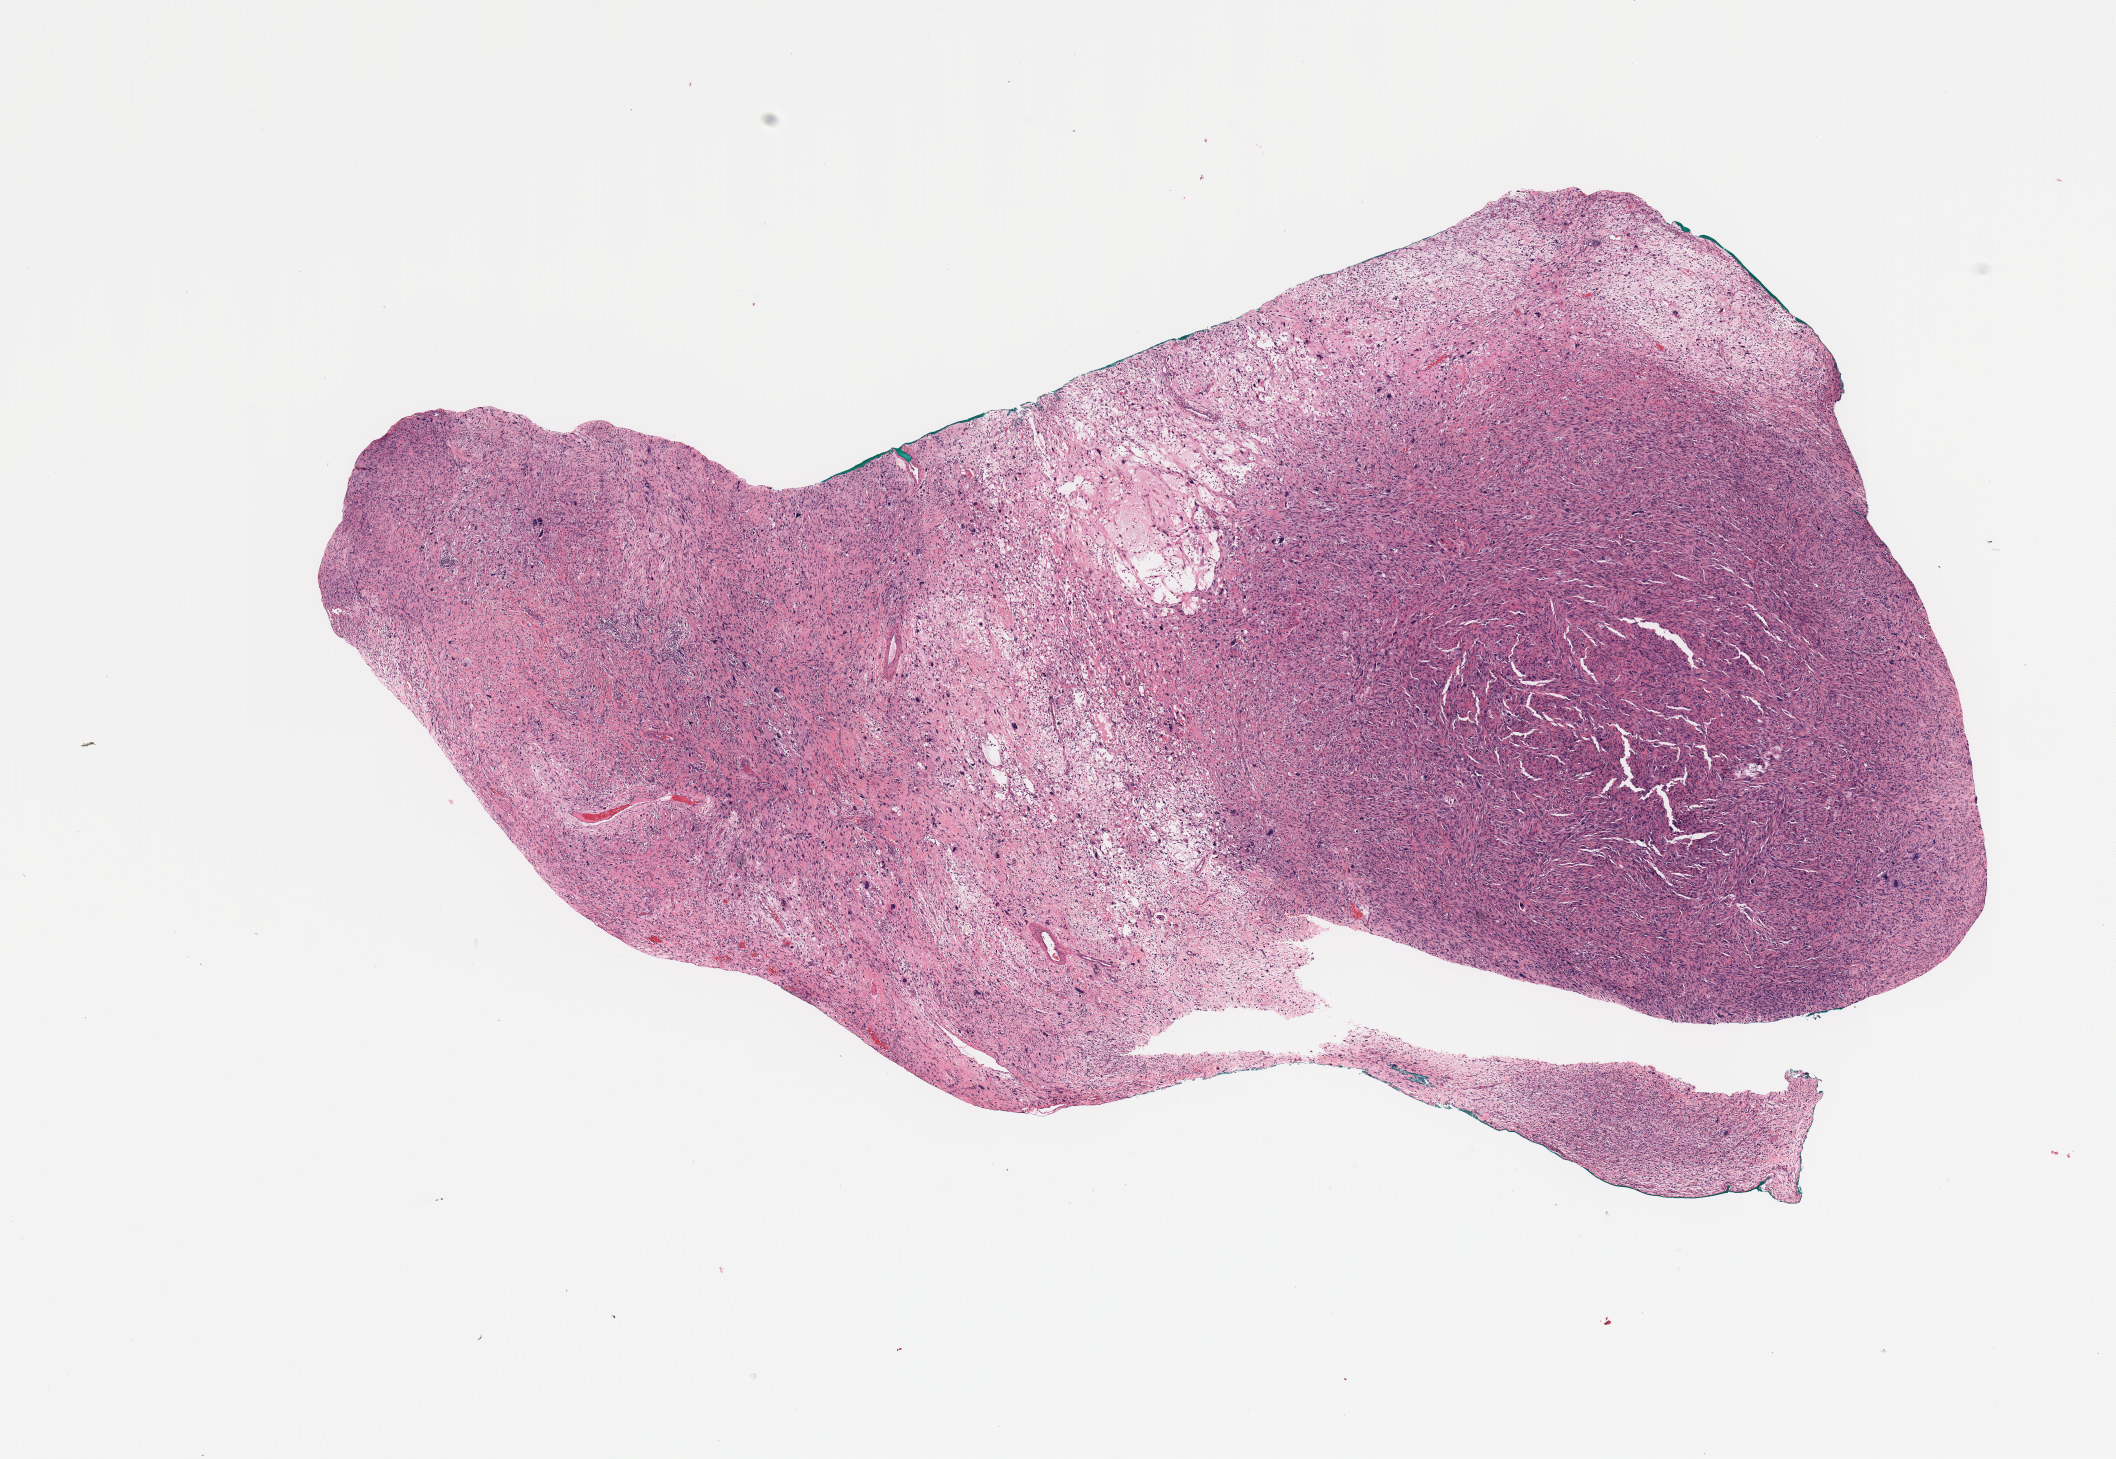
H&E whole-slide image, a low-resolution overview of the entire scanned area, about 16.7 x 11.5 mm, tumour tissue sample. Patient: male, age 60 years.
Primary tumour site (as recorded): lower extremity. Patient diagnosis (cohort enrolment): sarcoma (site not recorded at cohort level).